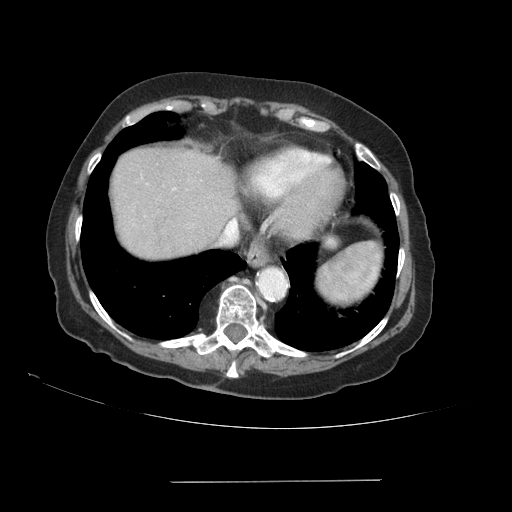
Contrast-enhanced abdominal CT (liver protocol), one axial slice. Slice 78 of 89 in the series (ordered by position). Reconstruction kernel STANDARD. 140 kVp. Soft-tissue window (W 400 / L 40 HU). 2.5 mm slice thickness. 512 × 512 image matrix, field of view 400 × 400 mm. From the clinical record (not read from this slice): diagnosis: hepatocellular carcinoma (patient treated with transarterial chemoembolisation; whether this scan precedes or follows treatment is not stated here); TNM stage (as recorded): Stage-IVA; Child-Pugh class: A; tumour differentiation: poorly differentiated.
Structures marked on this image (semi-automatically segmented with operator editing):
- liver parenchyma outside the tumour (the mass and vessels are separate outlines, so this box may not span the whole liver): bounding box [x1, y1, x2, y2] px = [110, 148, 238, 258]